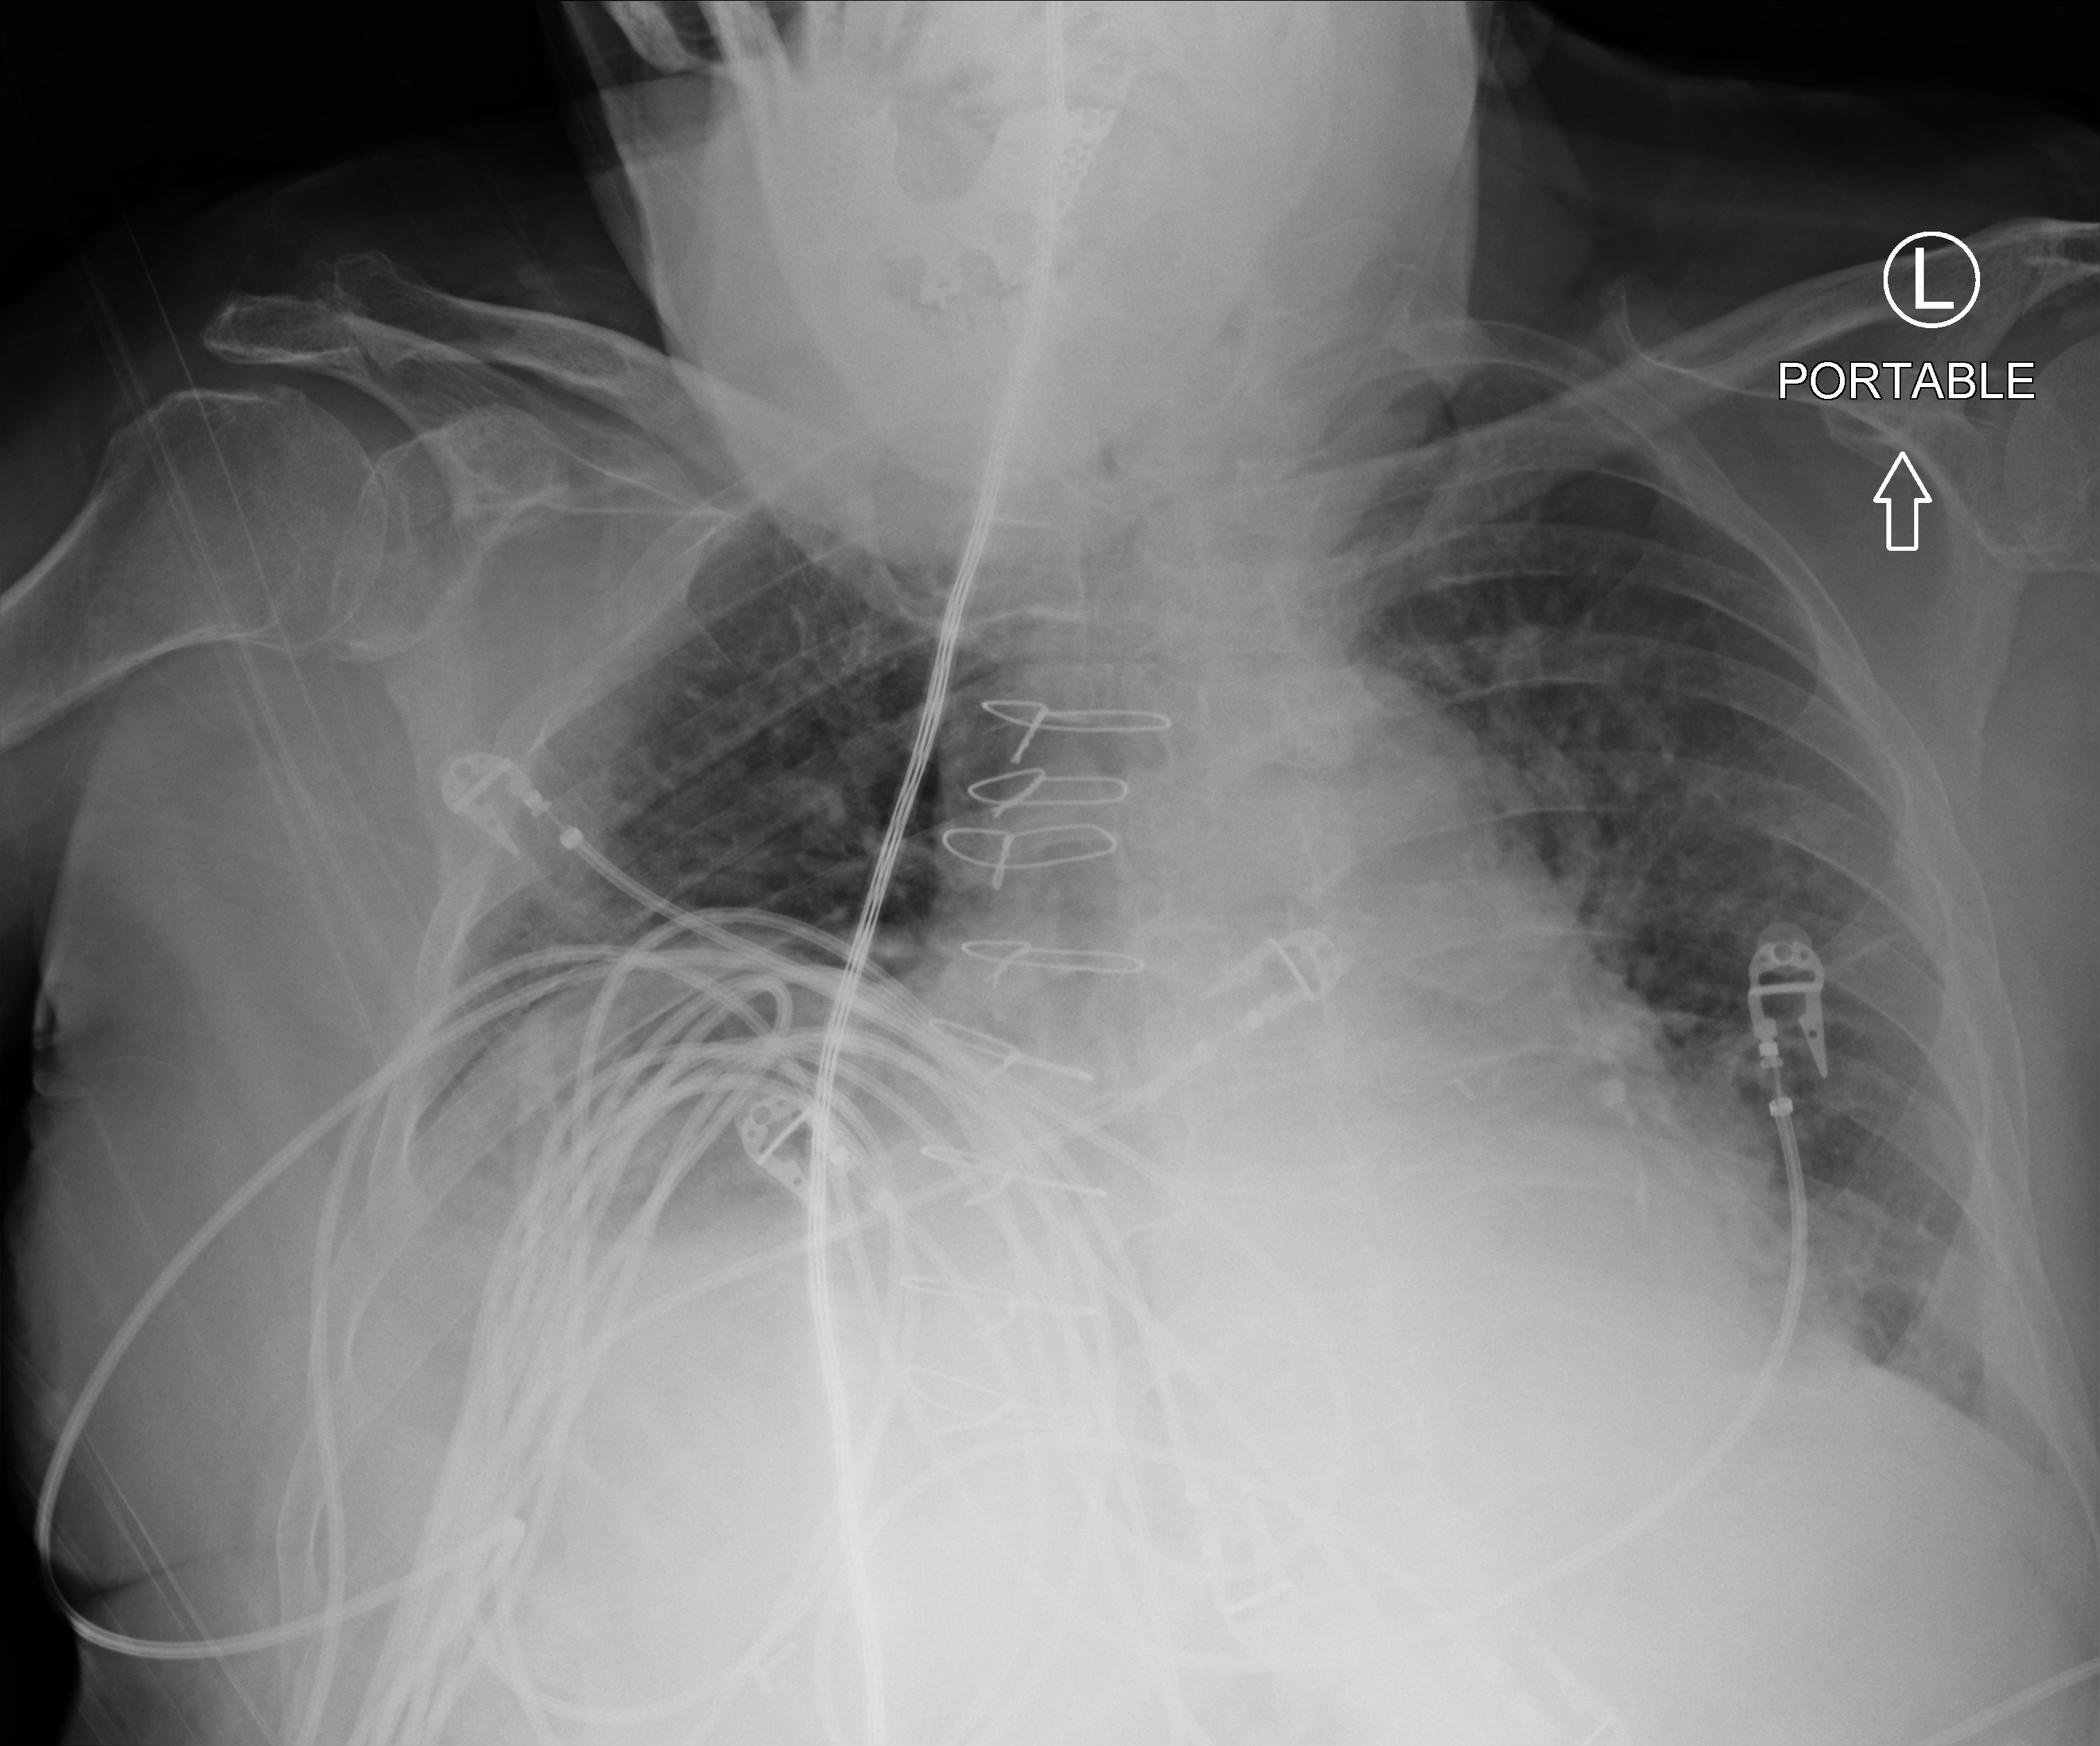
Bedside chest radiograph (computed radiography), anteroposterior (AP) projection. Male patient hospitalised with COVID-19, age 75–90 years.
From the hospital-stay record, not from the radiograph (when in the stay this image was taken is not recorded): mechanically ventilated during this hospital stay: no; diabetes (admission record): no.